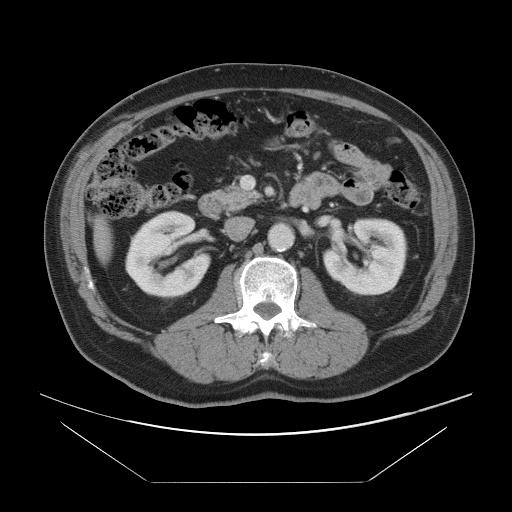
Contrast-enhanced abdominal CT, one axial slice. Slice 34 of 97 in the series (ordered by position). 120 kVp. Intravenous contrast given. Soft-tissue window (W 400 / L 40 HU). 5 mm slice thickness. 512 × 512 image matrix, field of view 442 × 442 mm. Male patient, age 62 years. From the clinical record (not read from this slice): diagnosis: colorectal cancer liver metastases, imaged before liver resection; multiple liver metastases: no; largest metastasis: 7 cm; disease in both lobes: yes.
Annotated regions visible in this slice (expert manual segmentation):
- liver: bounding box (x1, y1, x2, y2) in pixels: (96, 224, 112, 258)
- planned liver remnant (the part of the liver to remain after resection): (96, 224, 112, 258)